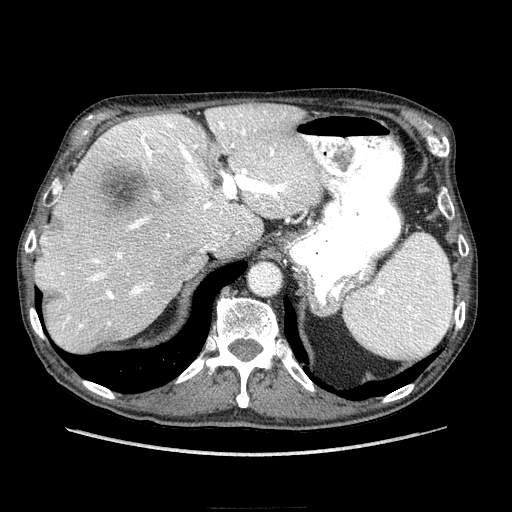
Contrast-enhanced abdominal CT (liver protocol), one axial slice. Position 167 of 218 along the scan axis. Reconstruction kernel STANDARD. 100 kVp. Soft-tissue window (W 400 / L 40 HU). 2.5 mm slice thickness. 512 × 512 image matrix, field of view 380 × 380 mm. Case-level facts recorded for this patient, not image findings: diagnosis: hepatocellular carcinoma (patient treated with transarterial chemoembolisation; whether this scan precedes or follows treatment is not stated here); TNM stage (as recorded): Stage-IIIA; Child-Pugh class: A; tumour differentiation: well differentiated; tumour nodularity: multinodular.
Outlined on this slice (semi-automatic segmentation, software-assisted and operator-edited):
- abdominal aorta: bounding box (x1, y1, x2, y2) in pixels: (251, 264, 280, 295)
- liver parenchyma outside the tumour (the mass and vessels are separate outlines, so this box may not span the whole liver): (36, 104, 305, 352)
- mass: (90, 158, 185, 220)
- liver vessels: (37, 109, 297, 342)